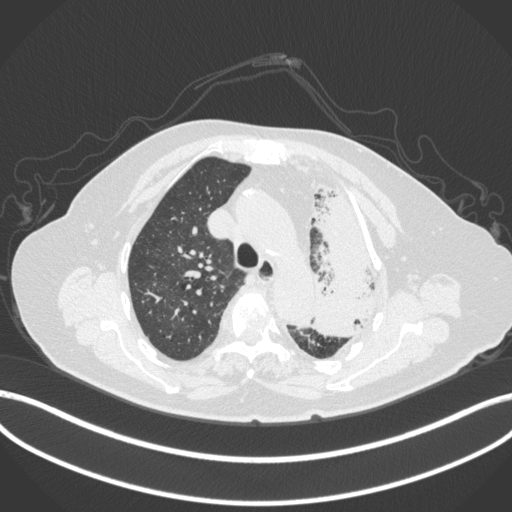
Chest CT, one axial slice. Position 290 of 399 along the scan axis. Reconstruction kernel B31f. 120 kVp. Lung window (W 1500 / L -600 HU). 512 × 512 image matrix. Patient: female, 75 years. Case-level facts recorded for this patient, not image findings: clinical TNM (as recorded): T3 N3 M1.
Outlined on this slice (rectangle marked by the reading radiologist):
- lung tumour (recorded histology: adenocarcinoma): bounding box [x1, y1, x2, y2] px = [304, 179, 390, 338]